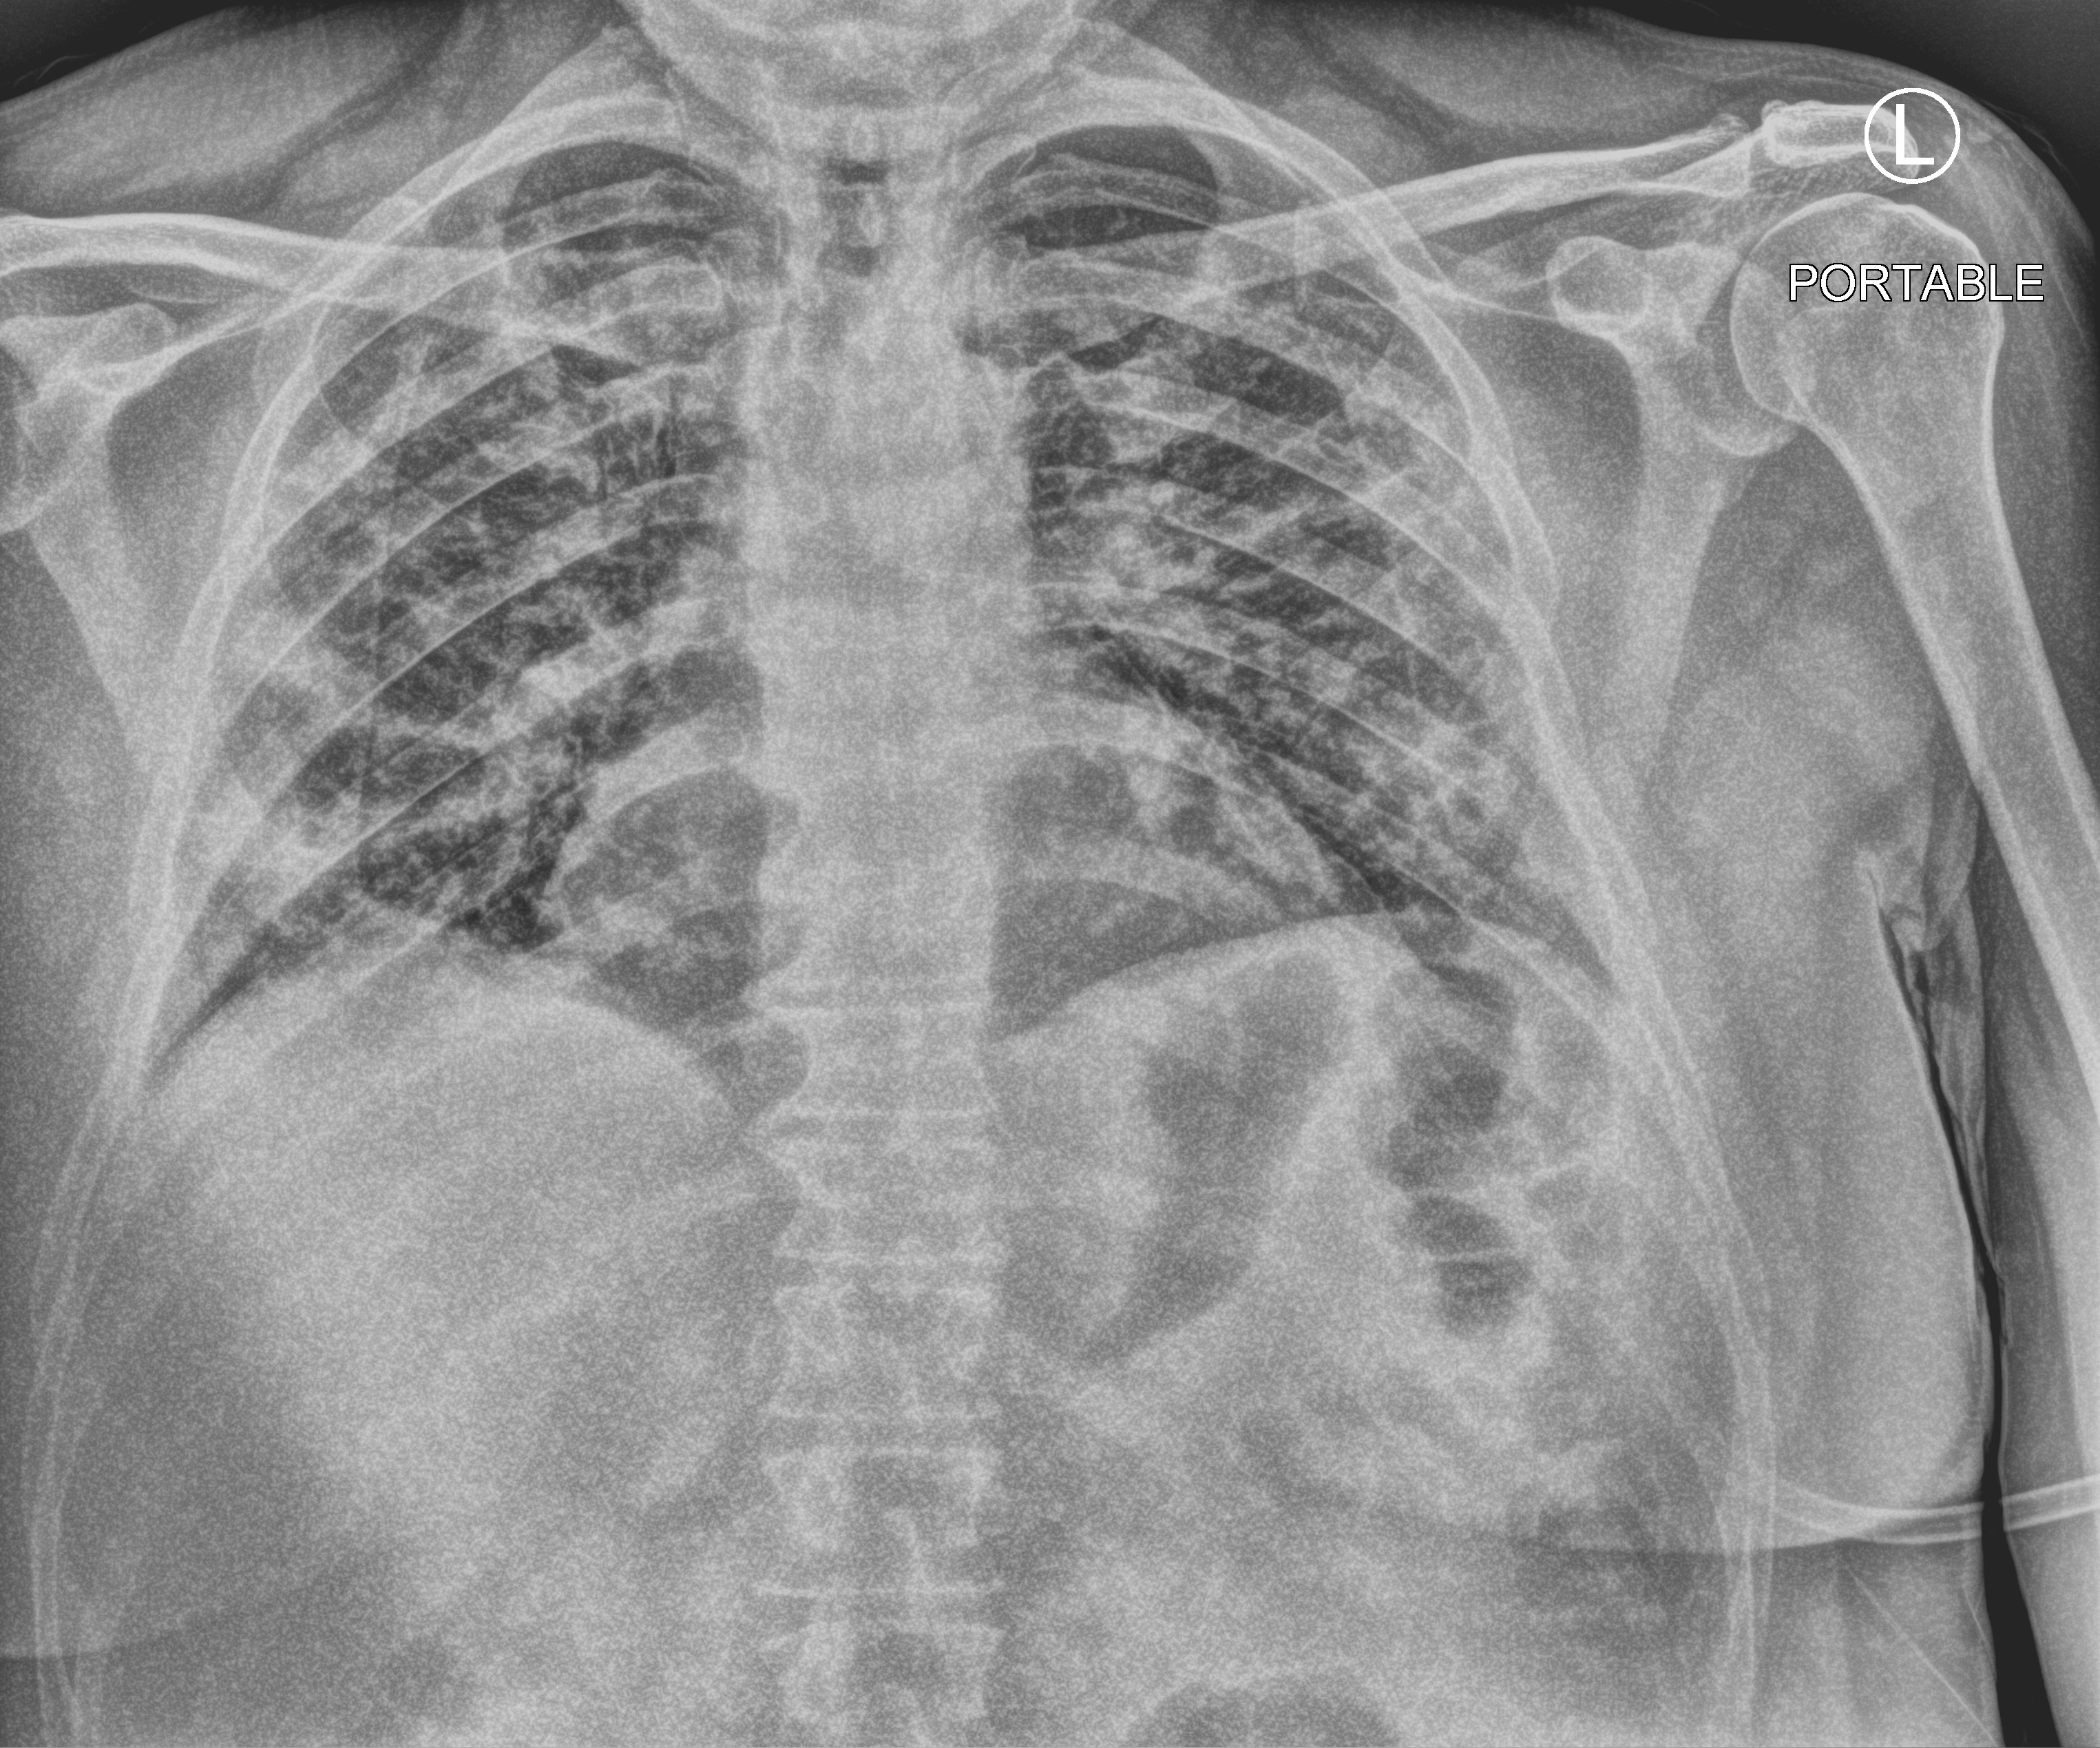
Chest X-ray (portable). Patient hospitalised with COVID-19; male, aged 18–59 years.
From the hospital-stay record, not from the radiograph (when in the stay this image was taken is not recorded): diabetes (admission record): no.